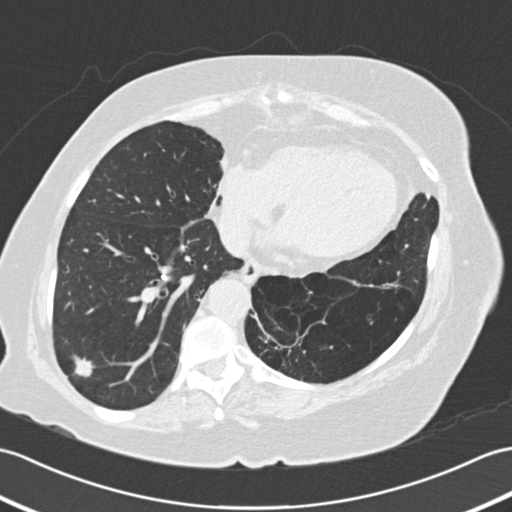
Low-dose screening chest CT, one axial slice. Slice 61 of 161 in the series (ordered by position). 120 kVp. Lung window (W 1500 / L -600 HU). 2 mm slice thickness. 512 × 512 image matrix, field of view 353 × 353 mm.
Structures marked on this image (outlined manually by an expert reader):
- lesion 1 (tumor, lower lobe of right lung): bounding box [x1, y1, x2, y2] px = [74, 356, 94, 377]